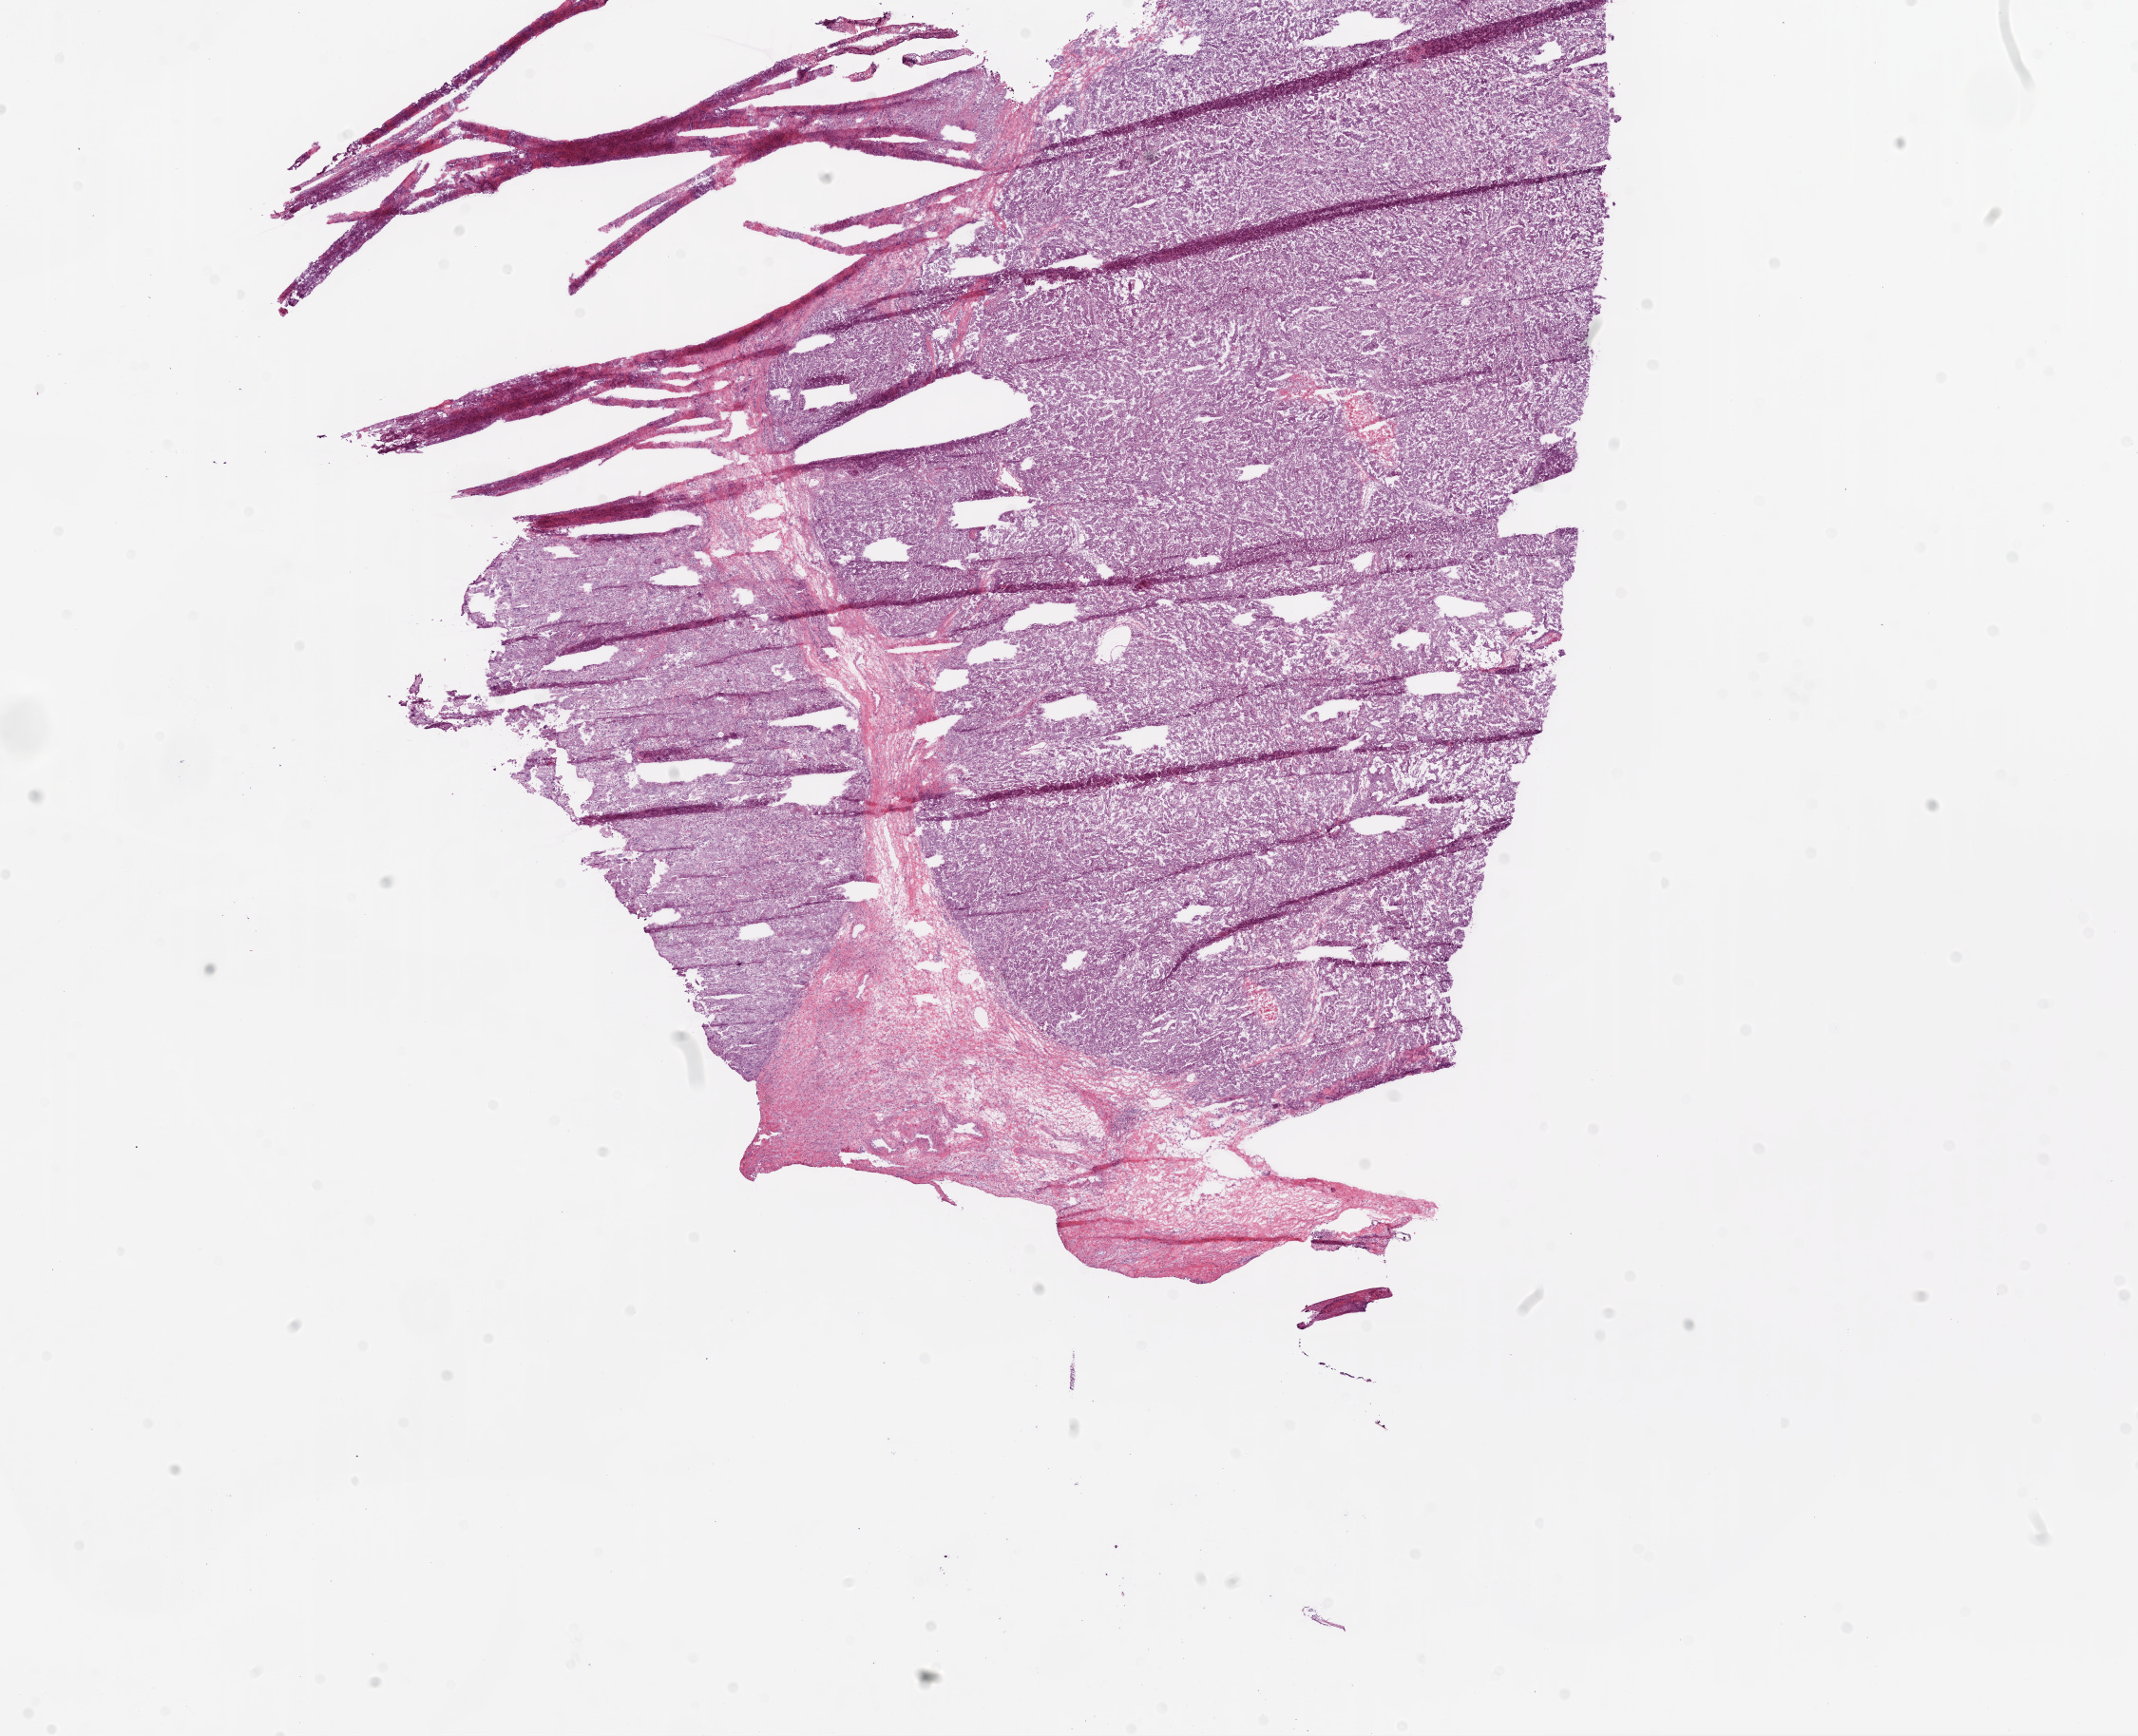
Digitized H&E tissue section (whole slide), a low-resolution overview of the entire scanned area, about 18.1 x 14.7 mm, frozen section, sample: primary tumour, ovary. Female, age 75 years at initial diagnosis. Histologic grade: G3 (poorly differentiated). Slide review estimates, as recorded: tumour cells 94%, tumour nuclei 95%, normal cells 0%, stromal cells 5%, necrosis 1%.
Pathologic diagnosis: Serous cystadenocarcinoma, NOS. Laterality: bilateral. FIGO stage: IV.